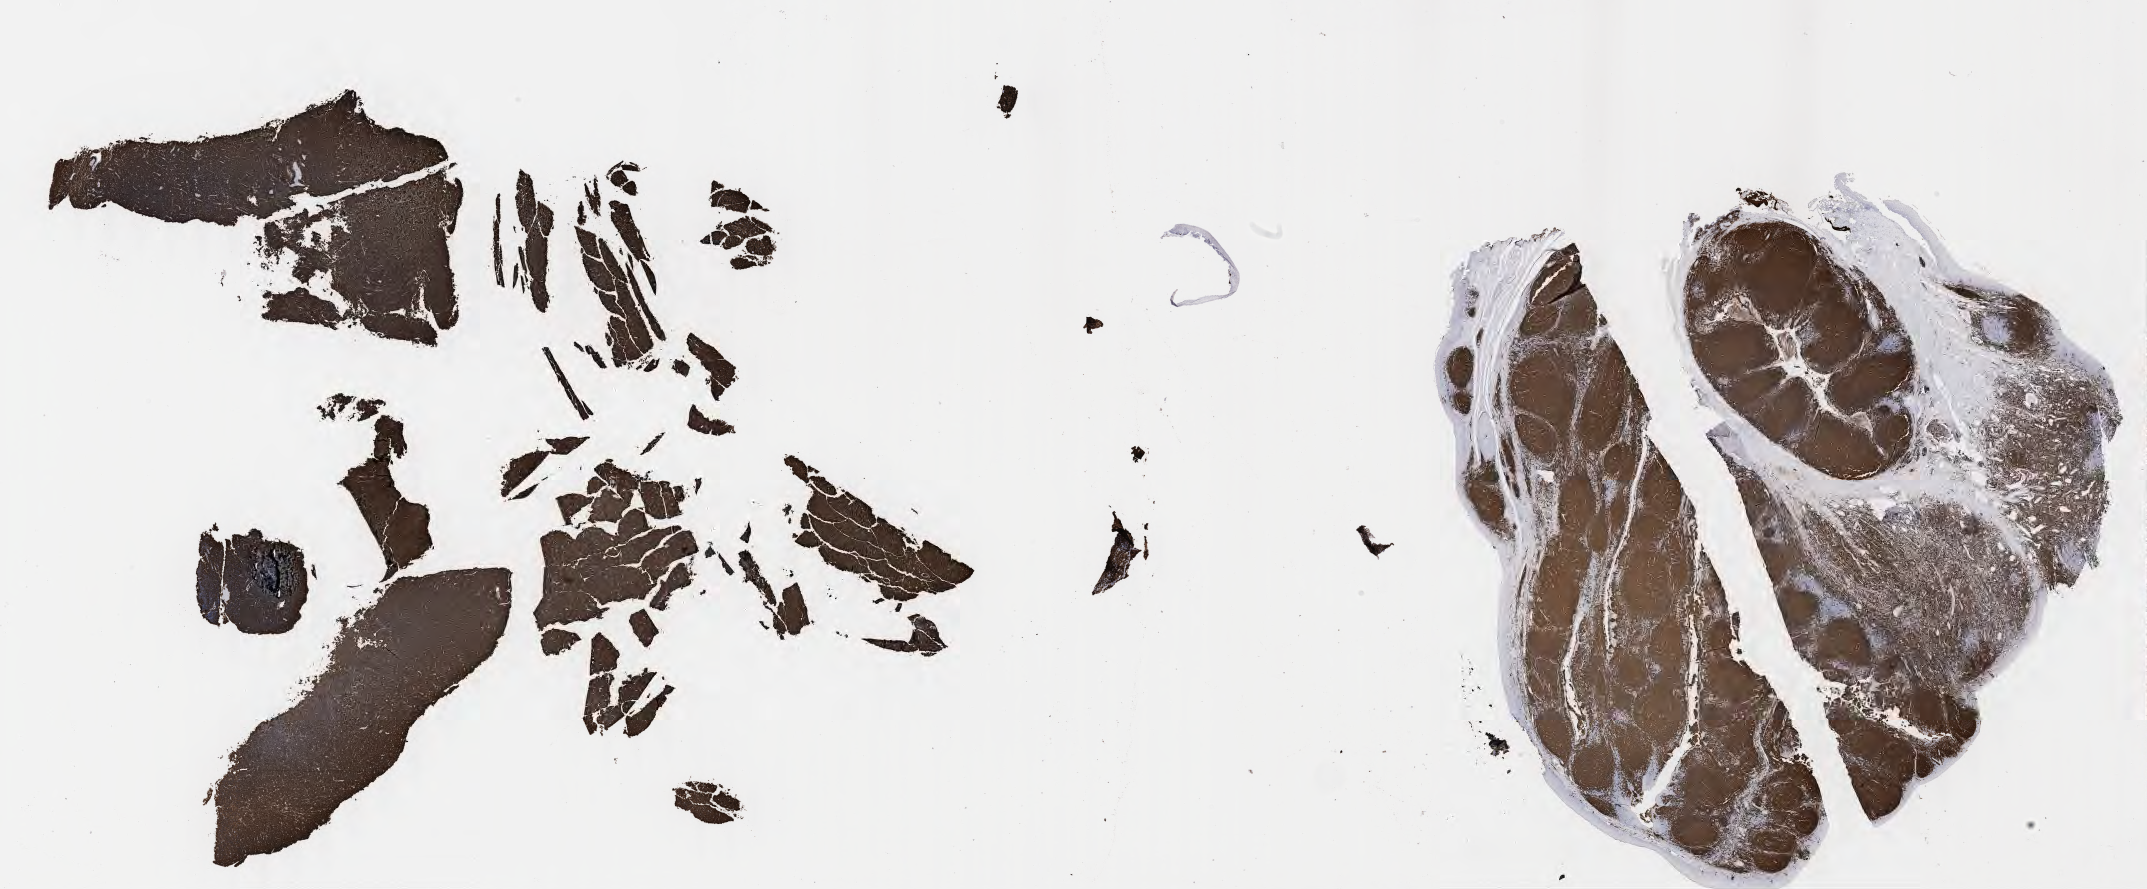
IHC for CD20, whole-slide image, a low-resolution overview of the entire scanned area, about 34.7 x 14.4 mm; specimen: tumor tissue. Male, age 9 years at initial diagnosis.
Diagnosis: Burkitt lymphoma, NOS.